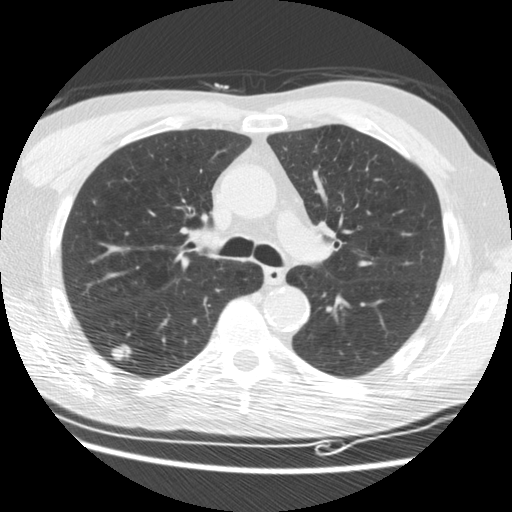
Low-dose screening chest CT, one axial slice; position 112 of 176 along the scan axis; reconstruction kernel STANDARD; 120 kVp; lung window (W 1500 / L -600 HU); 2.5 mm slice thickness; 512 × 512 image matrix.
Annotated regions visible in this slice (manually delineated by an expert):
- lesion 1 (tumor, lower lobe of right lung): box from (x=111, y=344) to (x=132, y=361) px